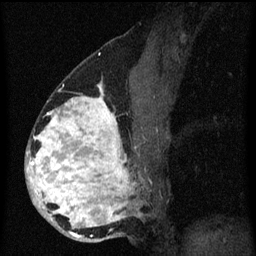
Breast MRI (dynamic contrast-enhanced), one sagittal slice; slice 34 of 60 in the series (ordered by position); dynamic contrast-enhanced series, image 2 of 3 at this slice position (ordered by acquisition); 1.5 T; TE 4.2 ms, TR 8.4 ms; 256 × 256 image matrix. Female patient, age 34 years. From the clinical record (not read from this slice): setting: breast cancer imaged before/during neoadjuvant chemotherapy; receptor status: HR-positive, HER2-negative.
Outlined on this slice (semi-automatically segmented with operator editing):
- analysis volume of interest (the breast-tissue region the enhancement analysis was run in; not a lesion): box from (x=26, y=58) to (x=157, y=243) px
- tumour enhancement mask (voxels above the 70 % enhancement threshold inside the analysis volume of interest): (x=26, y=84)–(x=133, y=239)